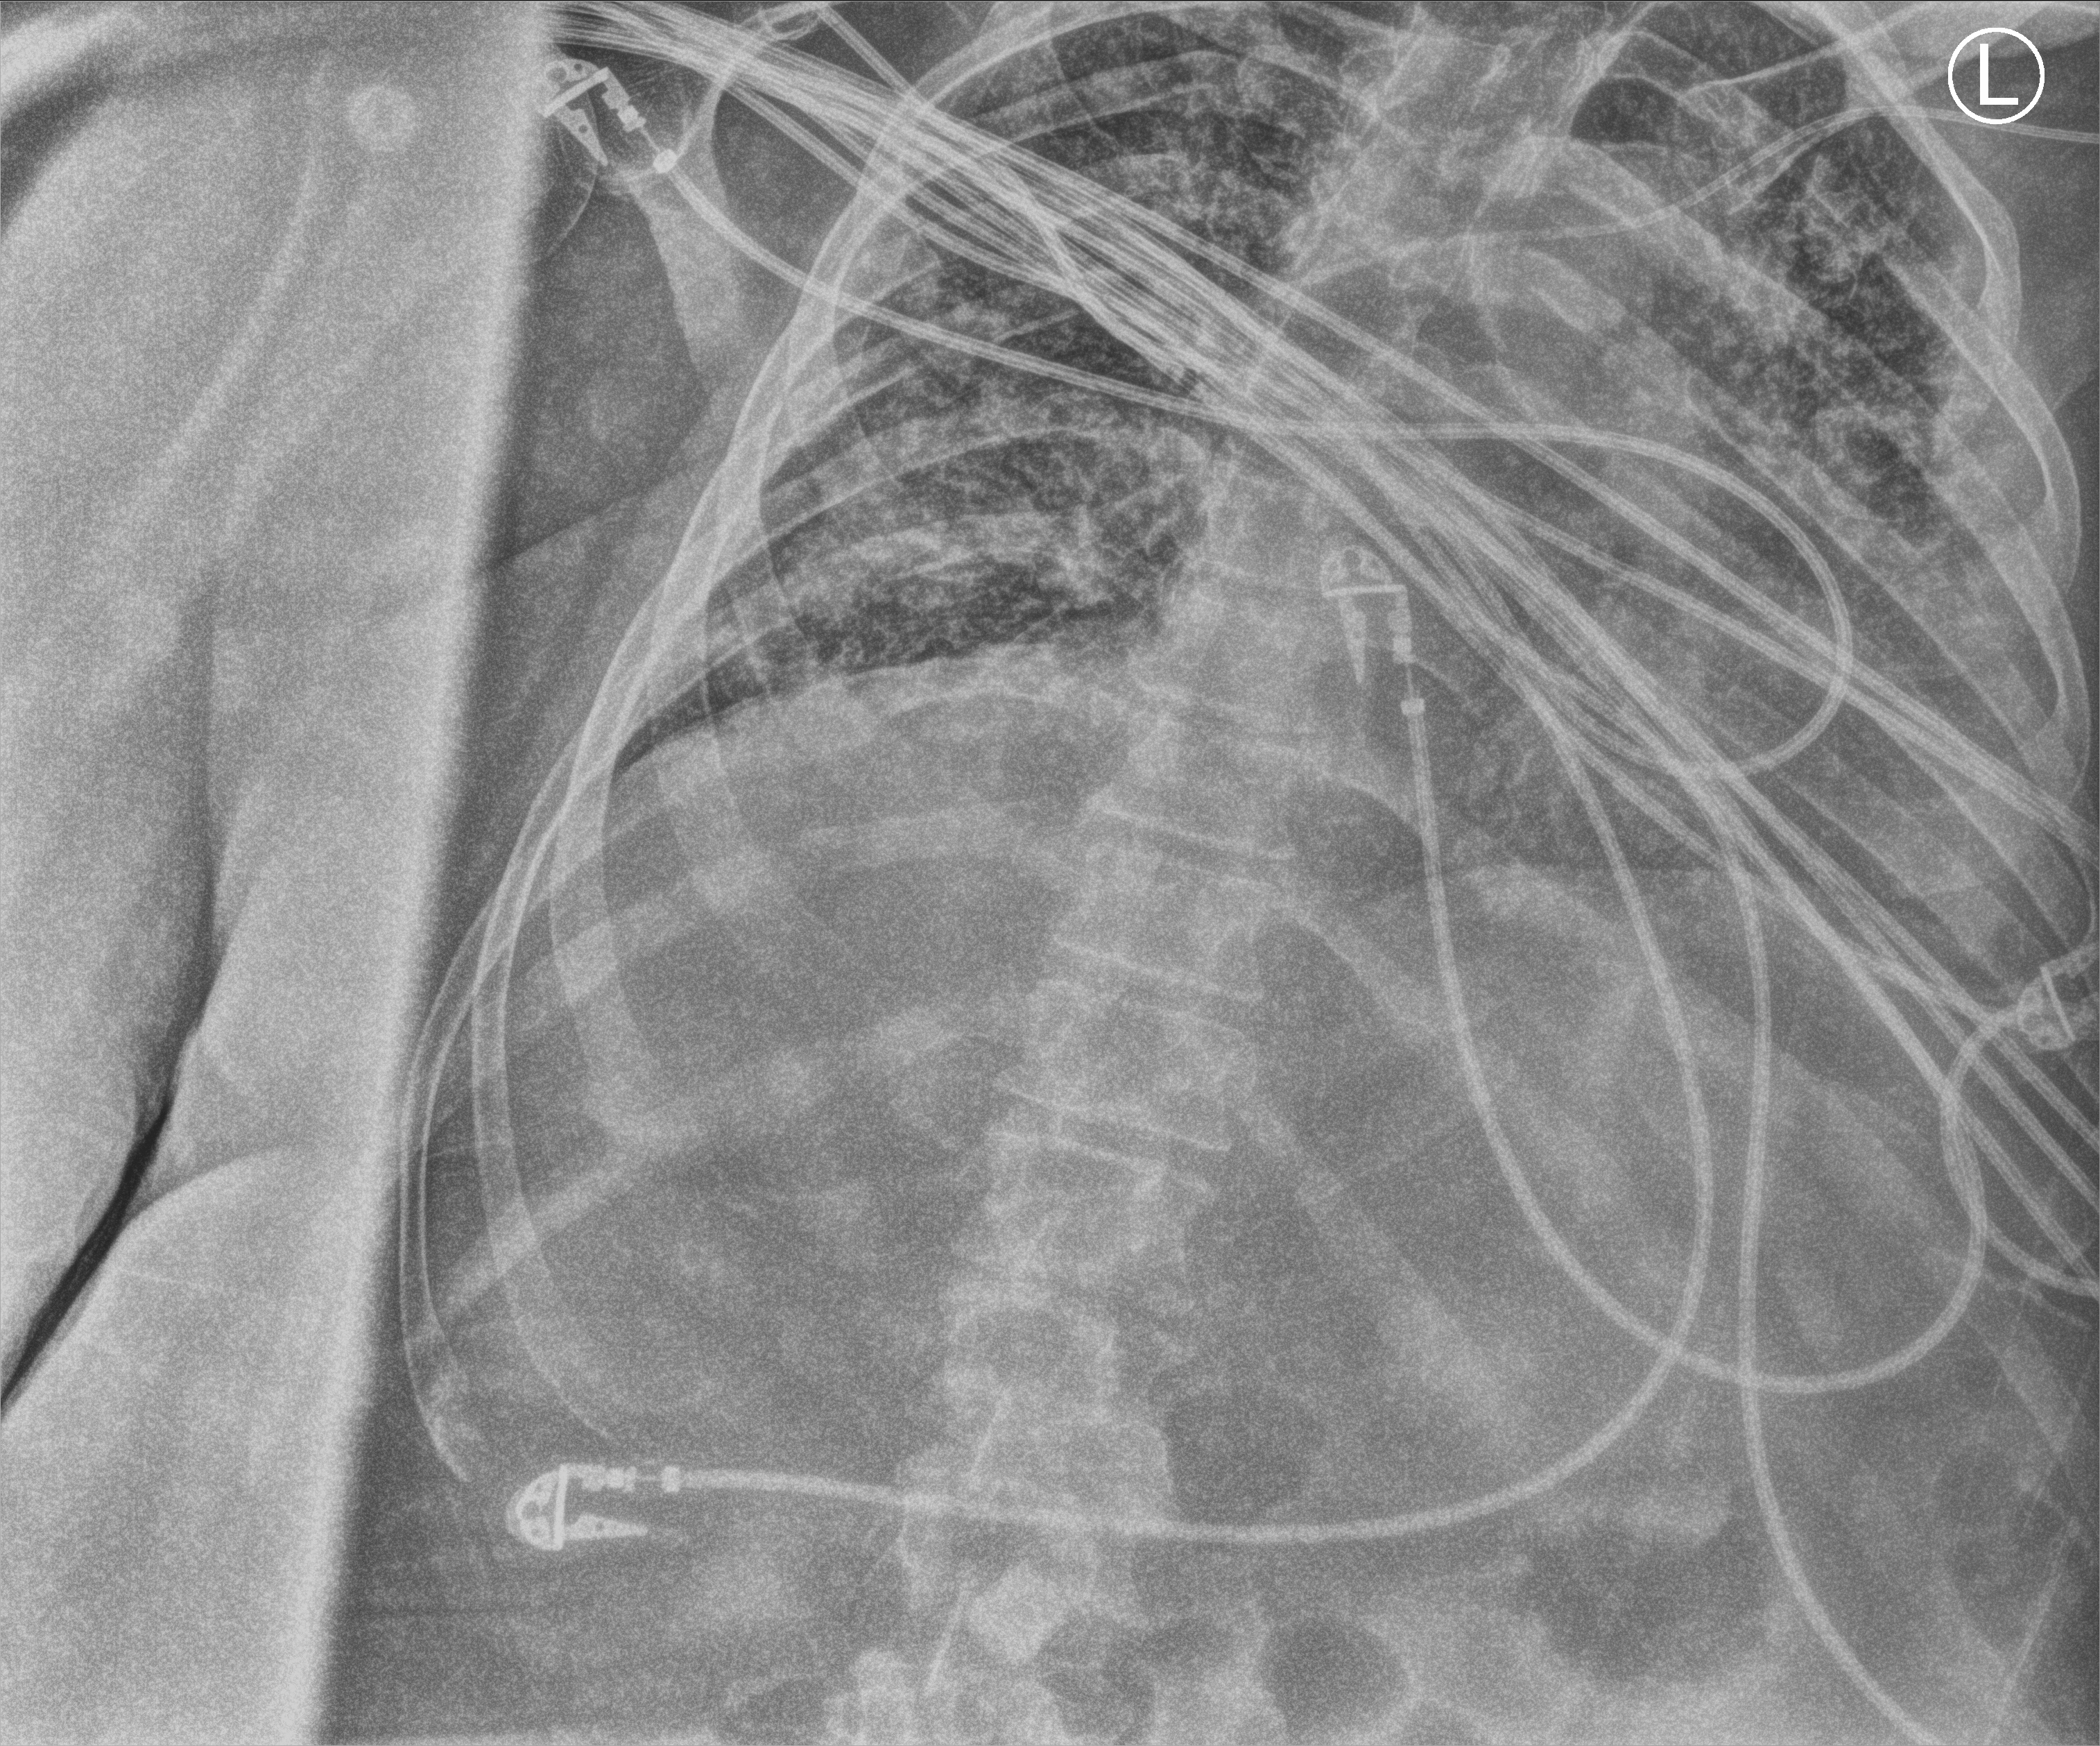
Bedside chest radiograph (computed radiography); anteroposterior (AP) projection. Male patient hospitalised with COVID-19, age 18–59 years.
From the hospital-stay record, not from the radiograph (when in the stay this image was taken is not recorded):
- length of hospital stay: 39 days